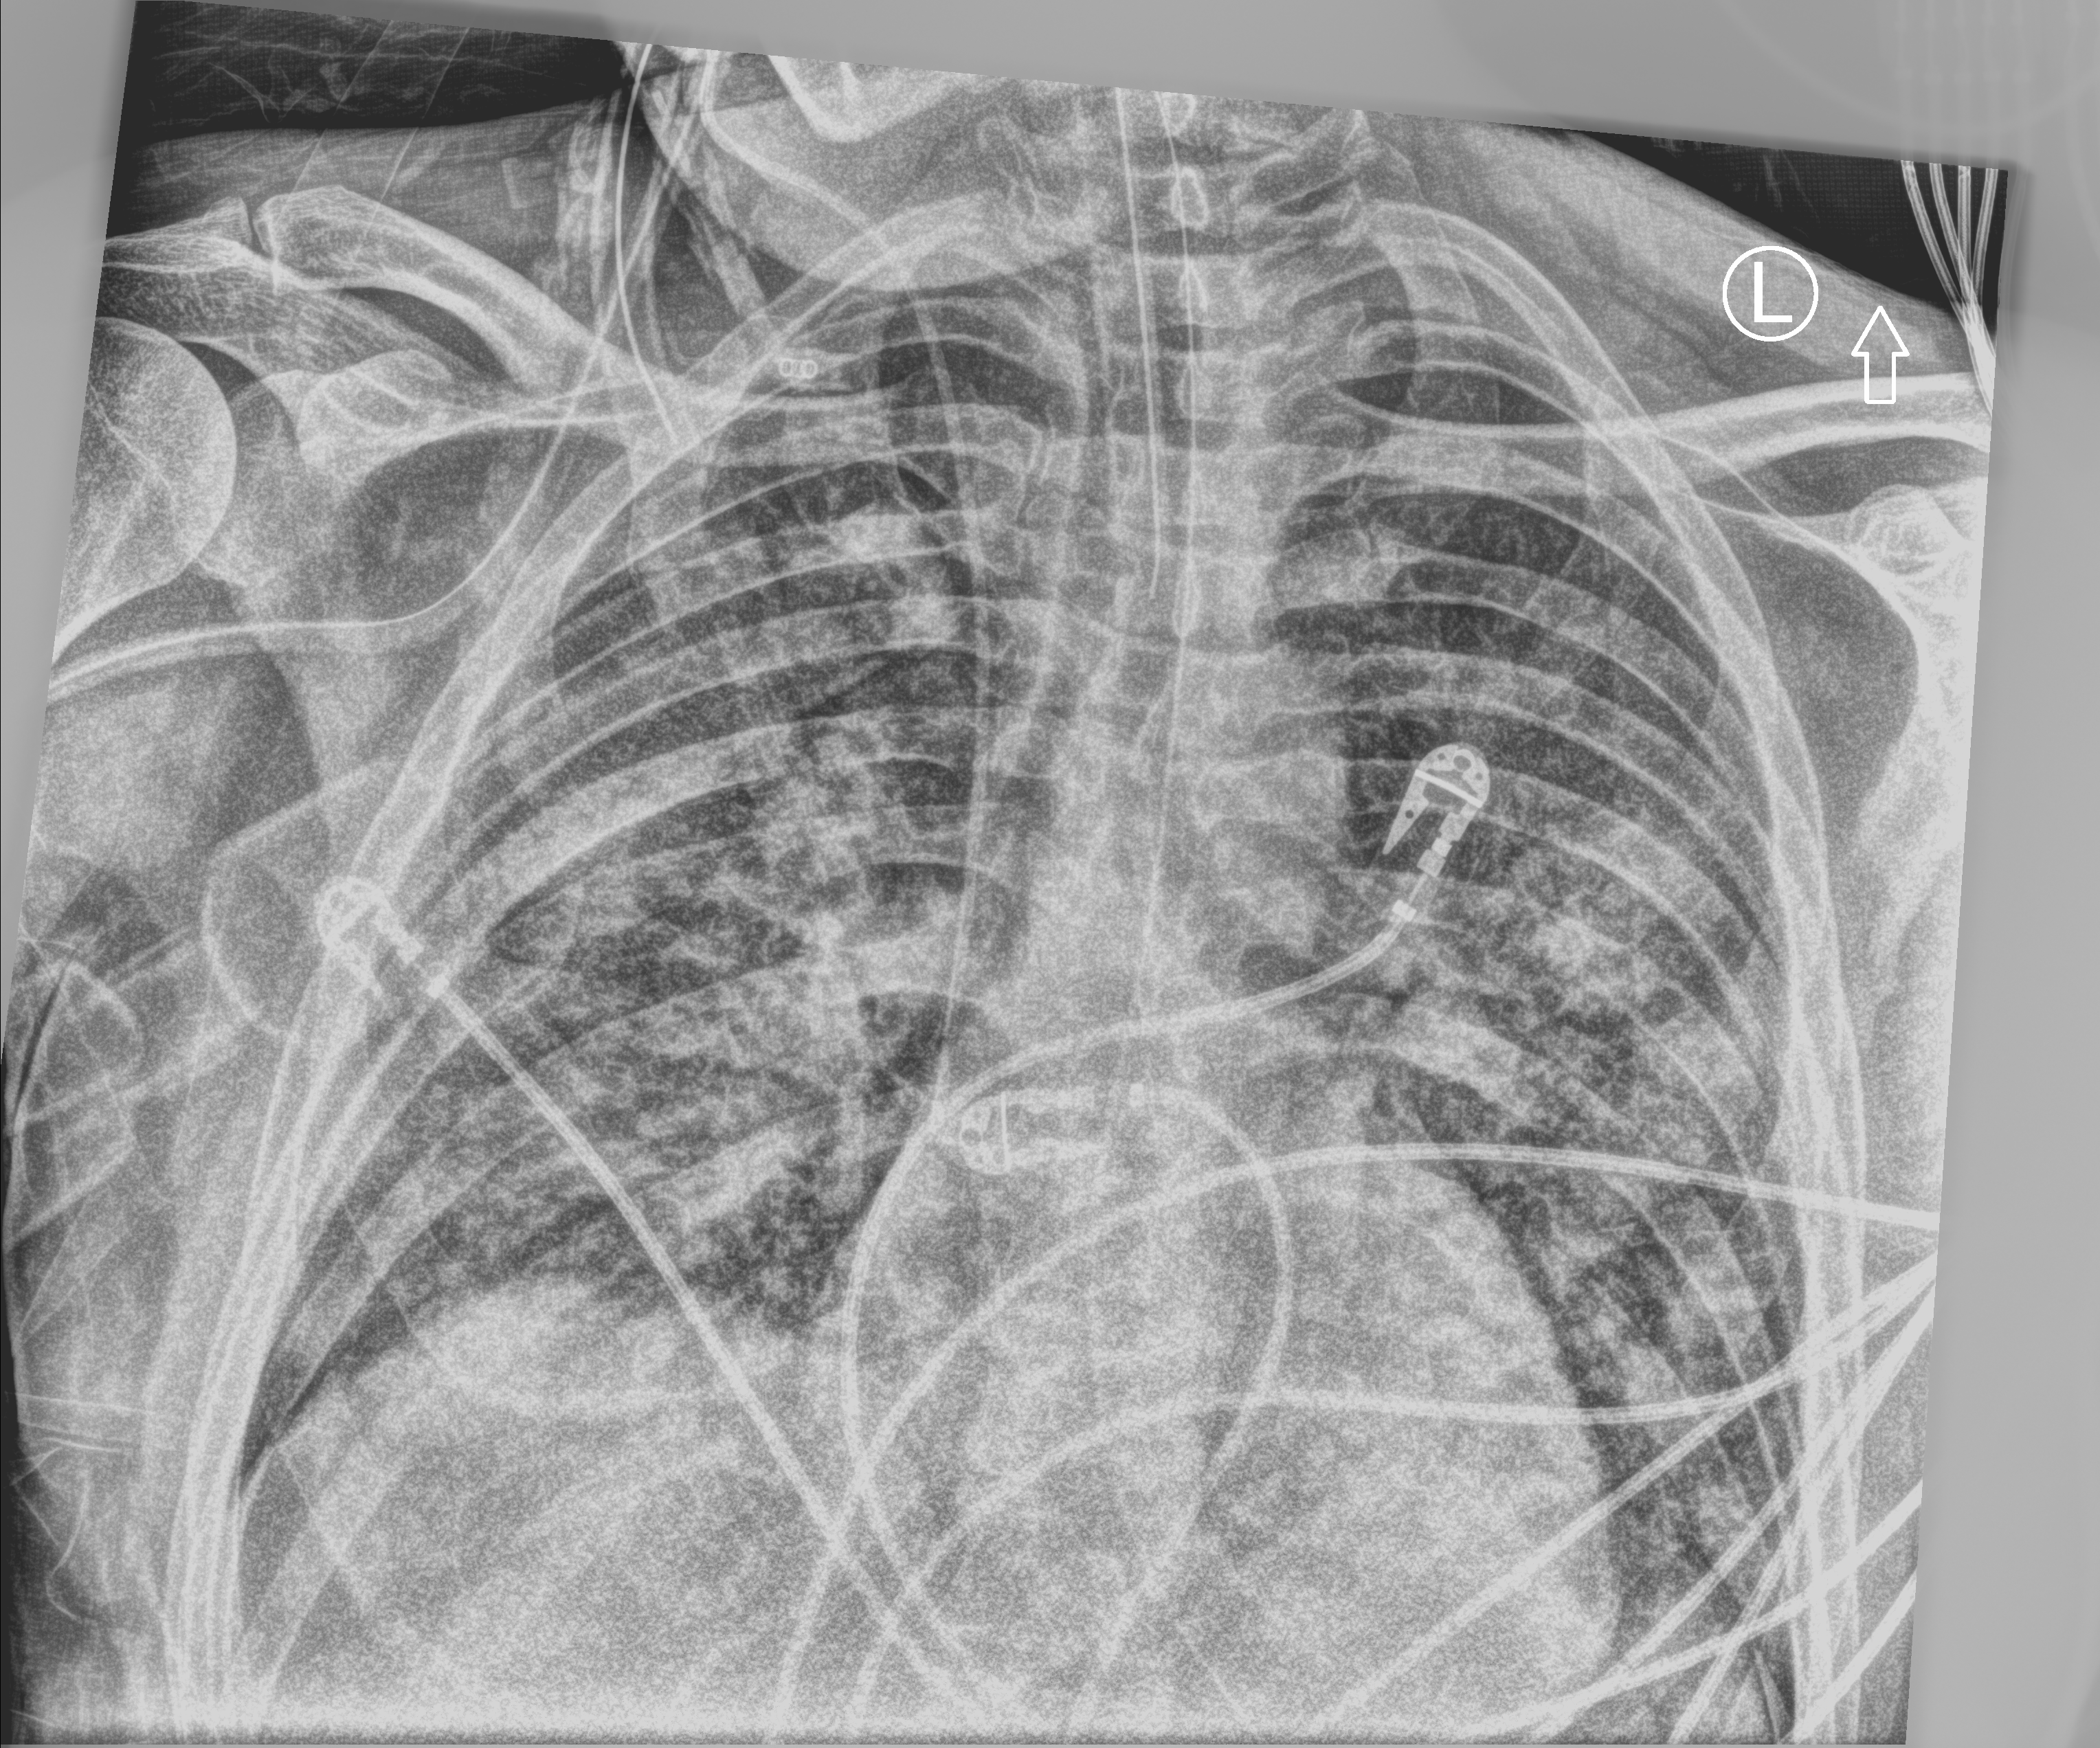
Chest X-ray (portable), anteroposterior (AP) projection. Patient hospitalised with COVID-19; male, aged 18–59 years.
Hospital-stay facts (about this admission, not read from this image; timing relative to this image not recorded):
- other chronic lung disease (admission record): no
- admitted to intensive care during this hospital stay: yes